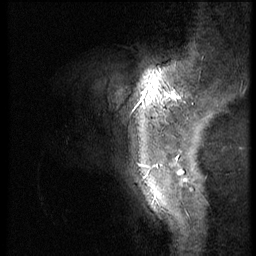
Breast MRI (dynamic contrast-enhanced), one sagittal slice; position 10 of 56 along the scan axis; 3 images stored at this slice position (order not interpretable as contrast timing); 1.5 T; TE 4.2 ms, TR 9 ms; 2.5 mm slice thickness; 256 × 256 image matrix, field of view 180 × 180 mm. Patient: female, 46 years. Case-level facts recorded for this patient, not image findings: setting: breast cancer imaged before/during neoadjuvant chemotherapy; receptor status: HER2-positive.
Annotated regions visible in this slice (semi-automatically segmented with operator editing):
- analysis volume of interest (the breast-tissue region the enhancement analysis was run in; not a lesion): bounding box (x1, y1, x2, y2) in pixels: (90, 68, 190, 143)
- tumour enhancement mask (voxels above the 140 % enhancement threshold inside the analysis volume of interest): (145, 92, 179, 100)